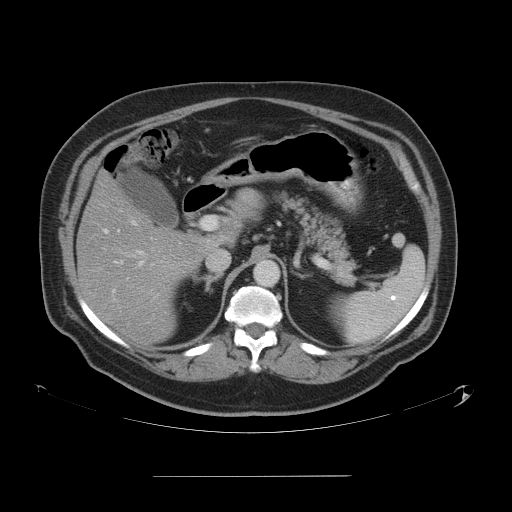
Contrast-enhanced abdominal CT, one axial slice; position 32 of 58 along the scan axis; 120 kVp; intravenous contrast given; soft-tissue window (W 400 / L 40 HU); 5 mm slice thickness; 512 × 512 image matrix. Male patient, age 63 years. Case-level facts recorded for this patient, not image findings: diagnosis: colorectal cancer liver metastases, imaged before liver resection; multiple liver metastases: no; largest metastasis: 4.2 cm; disease in both lobes: no.
Structures marked on this image (outlined manually by an expert reader):
- hepatic veins: bounding box <112,255,136,294> (left, top, right, bottom; pixels)
- liver: <78,174,218,342>
- planned liver remnant (the part of the liver to remain after resection): <78,187,202,342>
- portal vein (with intrahepatic branches): <104,229,160,293>